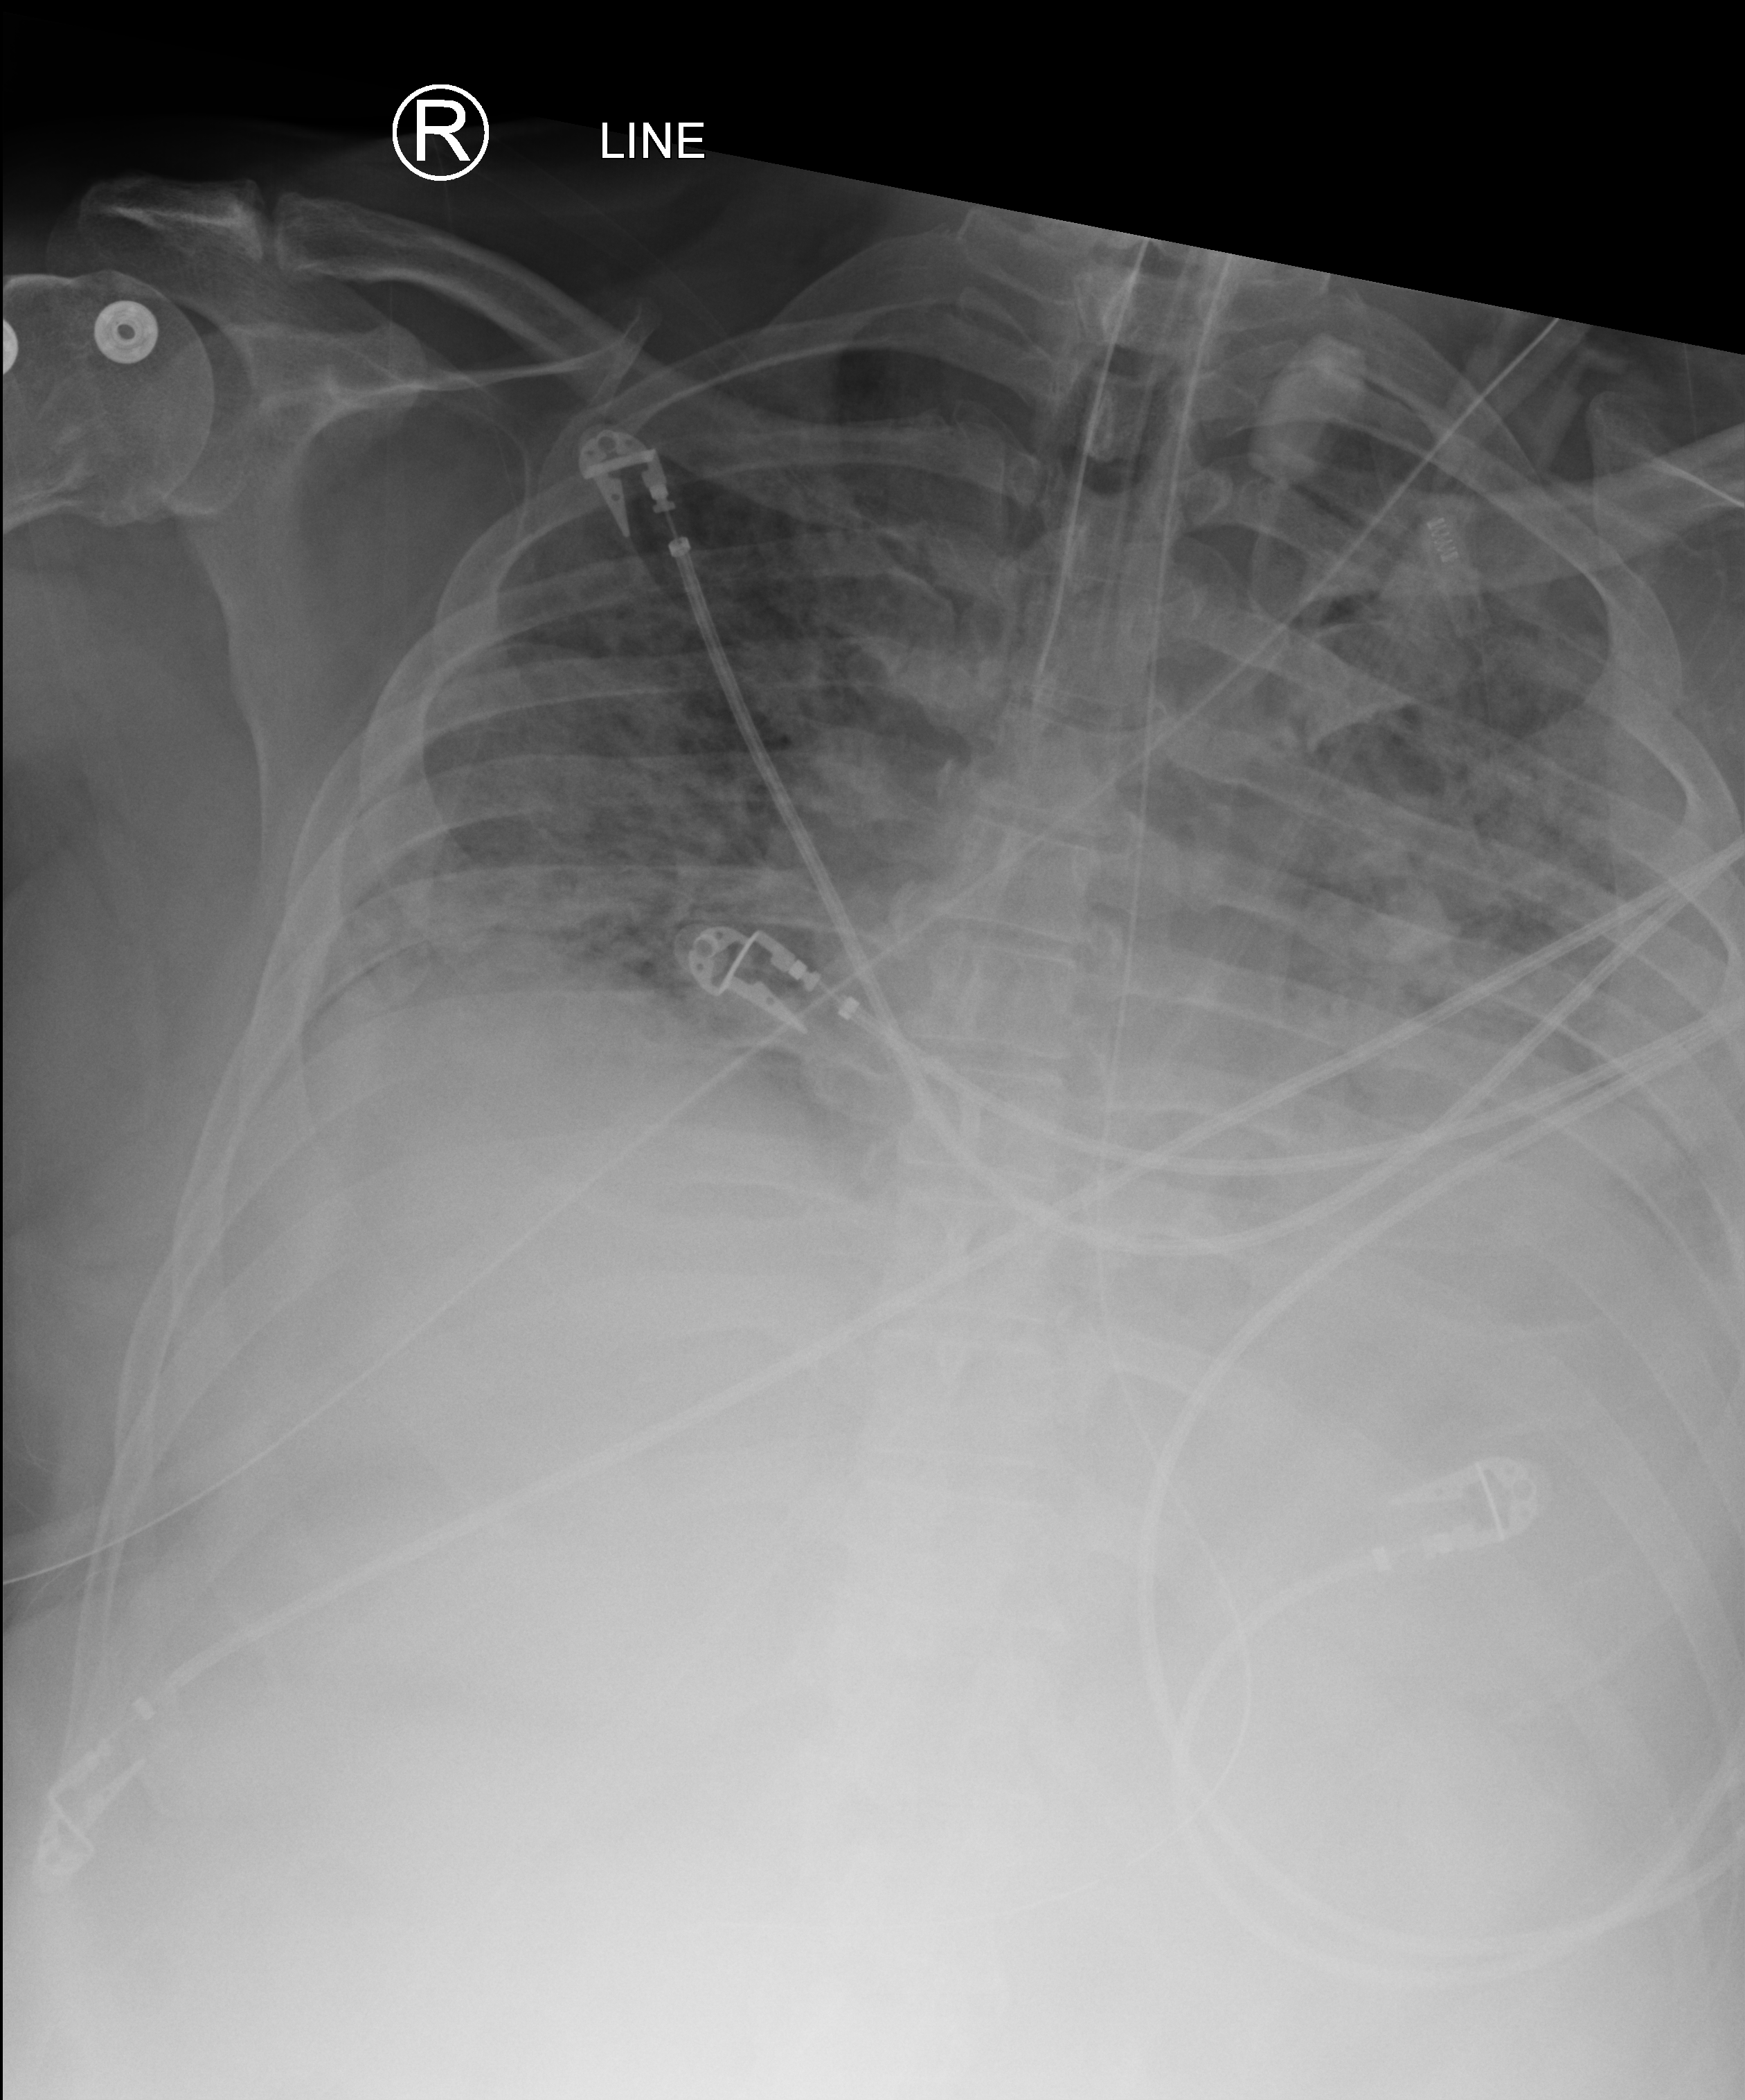
Portable chest radiograph; anteroposterior (AP) projection. Patient hospitalised with COVID-19; male, aged 18–59 years.
Admission-level facts for this patient (not findings on this image; timing relative to this image not recorded):
- diabetes (admission record): no
- smoking status (admission record): never
- admitted to intensive care during this hospital stay: yes